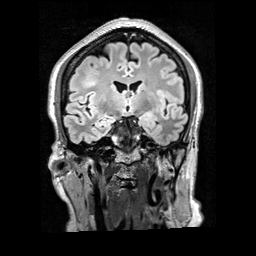
Brain MRI from a brain-tumour surgery series, one coronal slice; slice 106 of 200 in the series (ordered by position); T2 FLAIR; 1 mm slice thickness; 256 × 256 image matrix. Case-level facts recorded for this patient, not image findings: histopathology: Glioblastoma; WHO grade: 4; IDH mutation: no; tumour location: Right Frontal.
Outlined on this slice (outlined manually by an expert reader):
- tumour: bounding box [x1, y1, x2, y2] px = [83, 72, 99, 88]